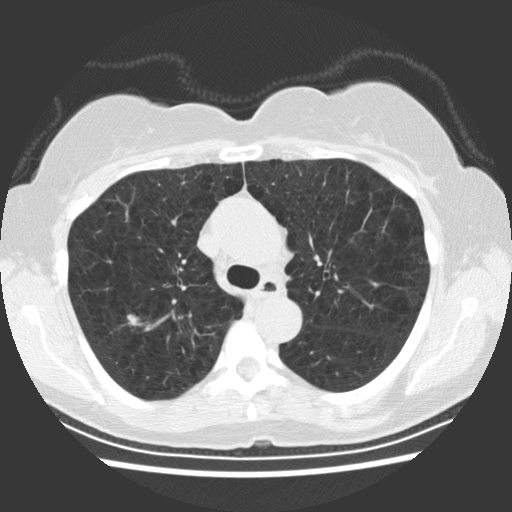
Chest CT (low-dose screening protocol), one axial image, baseline annual screen, lung window (W 1500 / L -600 HU), slice 69 of 234 in the series, 512 × 512 image matrix. Female participant, aged 66 years at enrolment. Former smoker at enrolment.
Expert reader's lesion annotation, bounding box (x1, y1, x2, y2) in pixels: (112, 299, 154, 339). The exam's reader record, not a measurement of the box and not confirmed to be the same lesion: non-calcified nodule or mass ≥4 mm, right upper lobe, 10 × 8 mm, smooth margins, soft tissue attenuation. Participant outcome: lung cancer diagnosed 54 days after this screen — squamous cell carcinoma, keratinizing, NOS, right upper lobe, poorly differentiated (G3), stage IA (AJCC 6th edition), 11 mm at pathology.